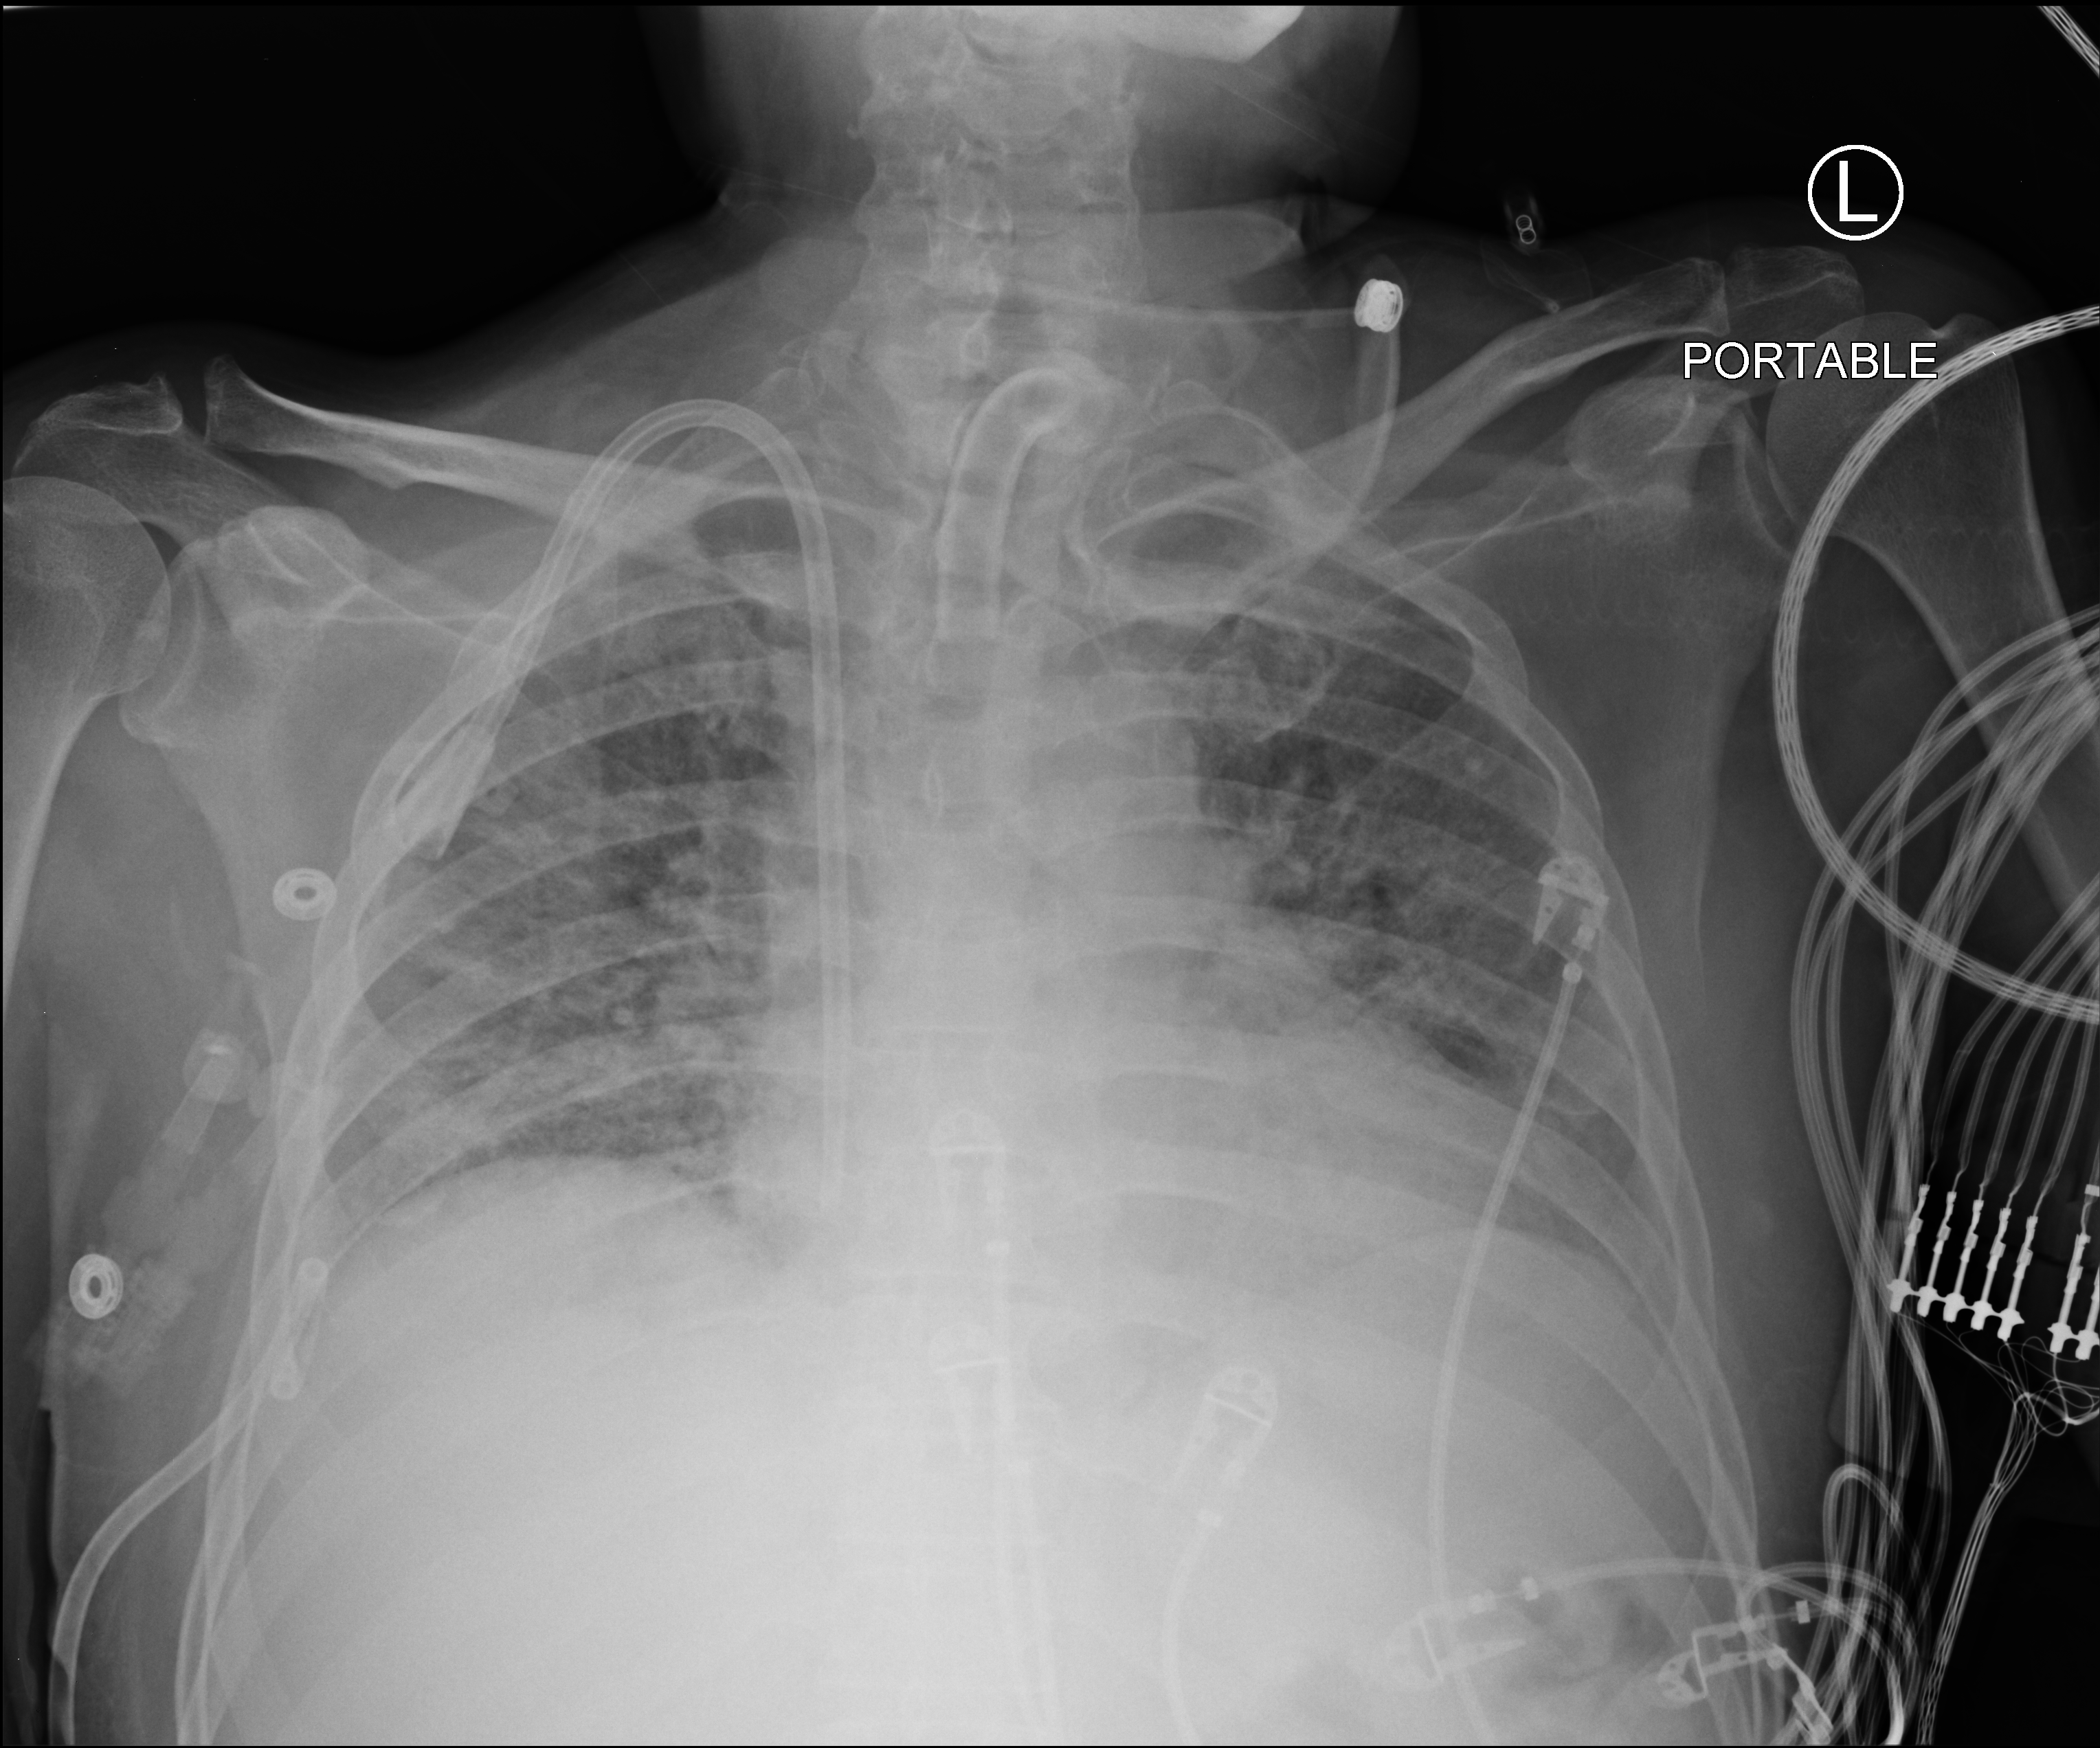
Portable chest radiograph; anteroposterior (AP) projection. Male patient hospitalised with COVID-19, age 18–59 years.
From the hospital-stay record, not from the radiograph (when in the stay this image was taken is not recorded):
- mechanically ventilated during this hospital stay: yes
- hypertension (admission record): no
- diabetes (admission record): no